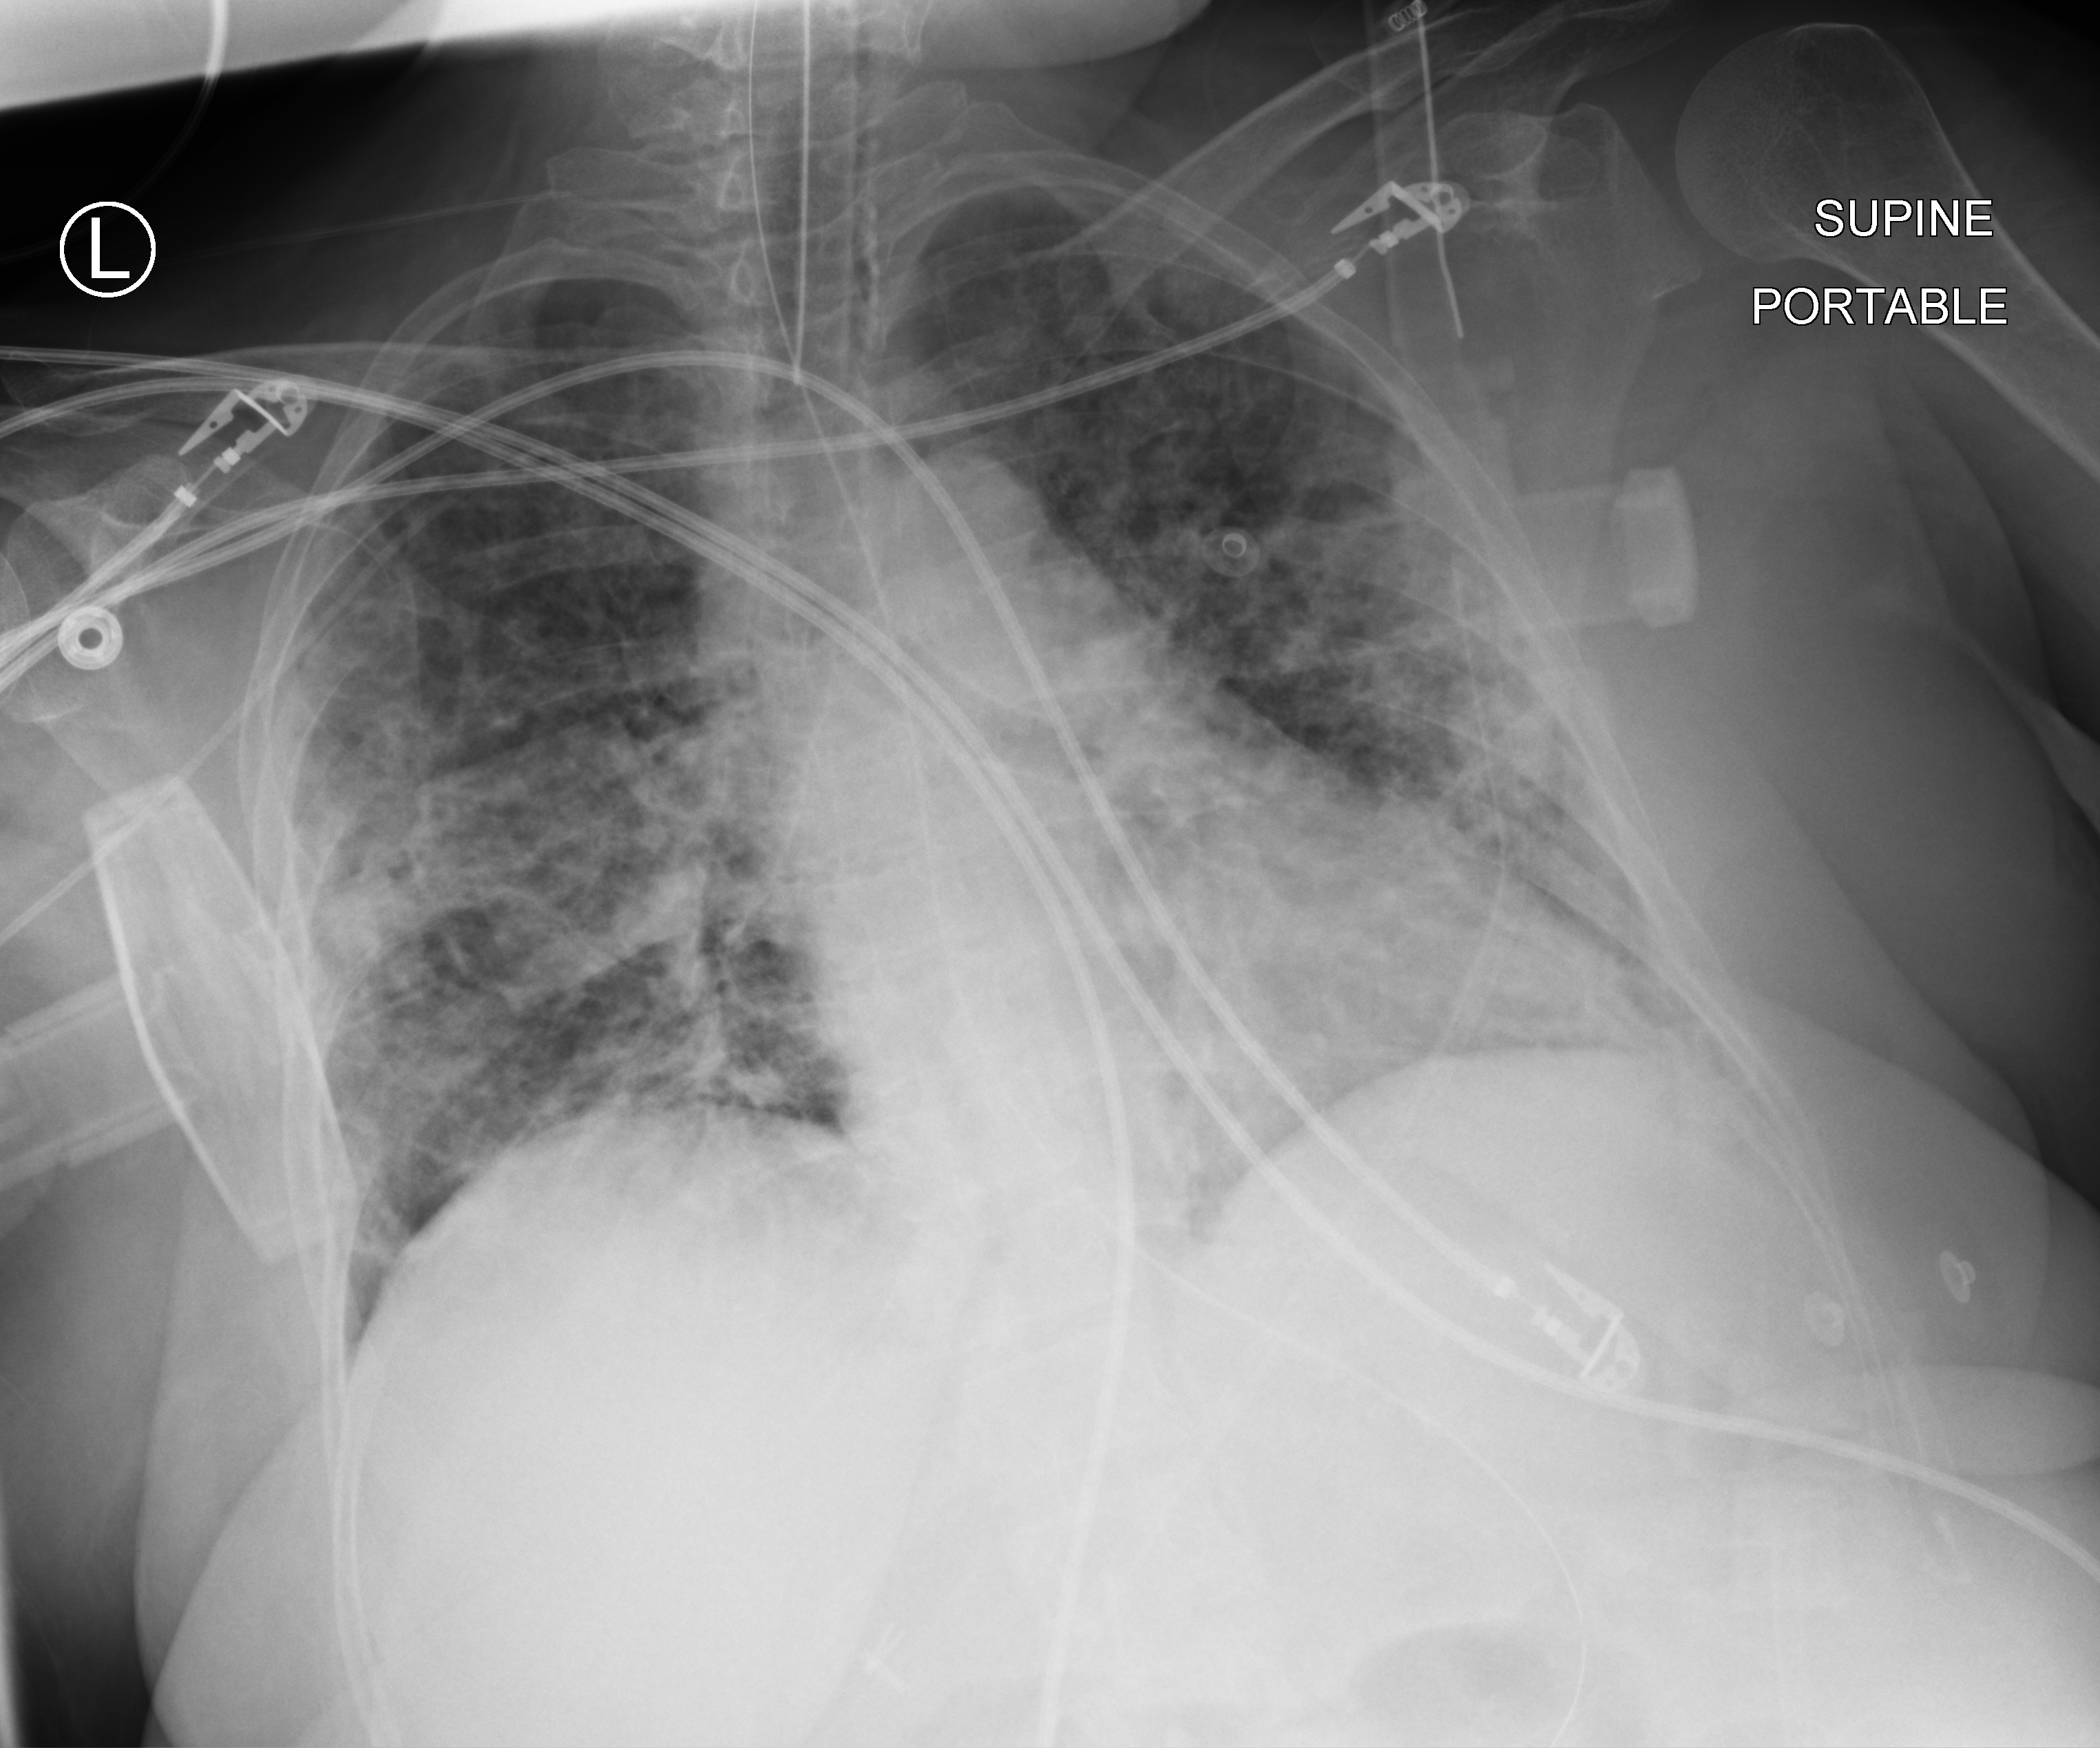
Bedside chest radiograph (computed radiography). Female patient hospitalised with COVID-19, age 18–59 years.
Hospital-stay facts (about this admission, not read from this image; timing relative to this image not recorded): mechanically ventilated during this hospital stay: yes.